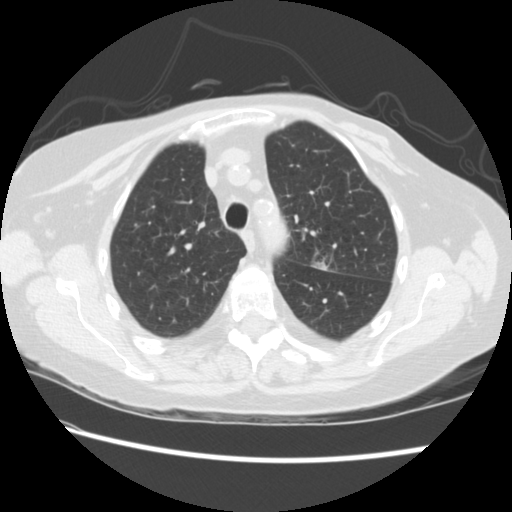
Axial slice from a low-dose chest CT screening exam, first (baseline) screen, lung window (W 1500 / L -600 HU), 2.5 mm slice thickness. Female, age 74 years at enrolment. Former smoker at enrolment.
Lesion marked by an expert reader, bounding box <296,234,346,279> (left, top, right, bottom; pixels). The screening reader recorded 2 non-calcified nodules or masses ≥4 mm on this exam (left upper lobe, right lower lobe); which of them this box marks is not recorded. Official screen result: positive, change unspecified: nodule(s) >= 4 mm or enlarging nodule(s), mass(es), or other non-specific abnormalities suspicious for lung cancer.